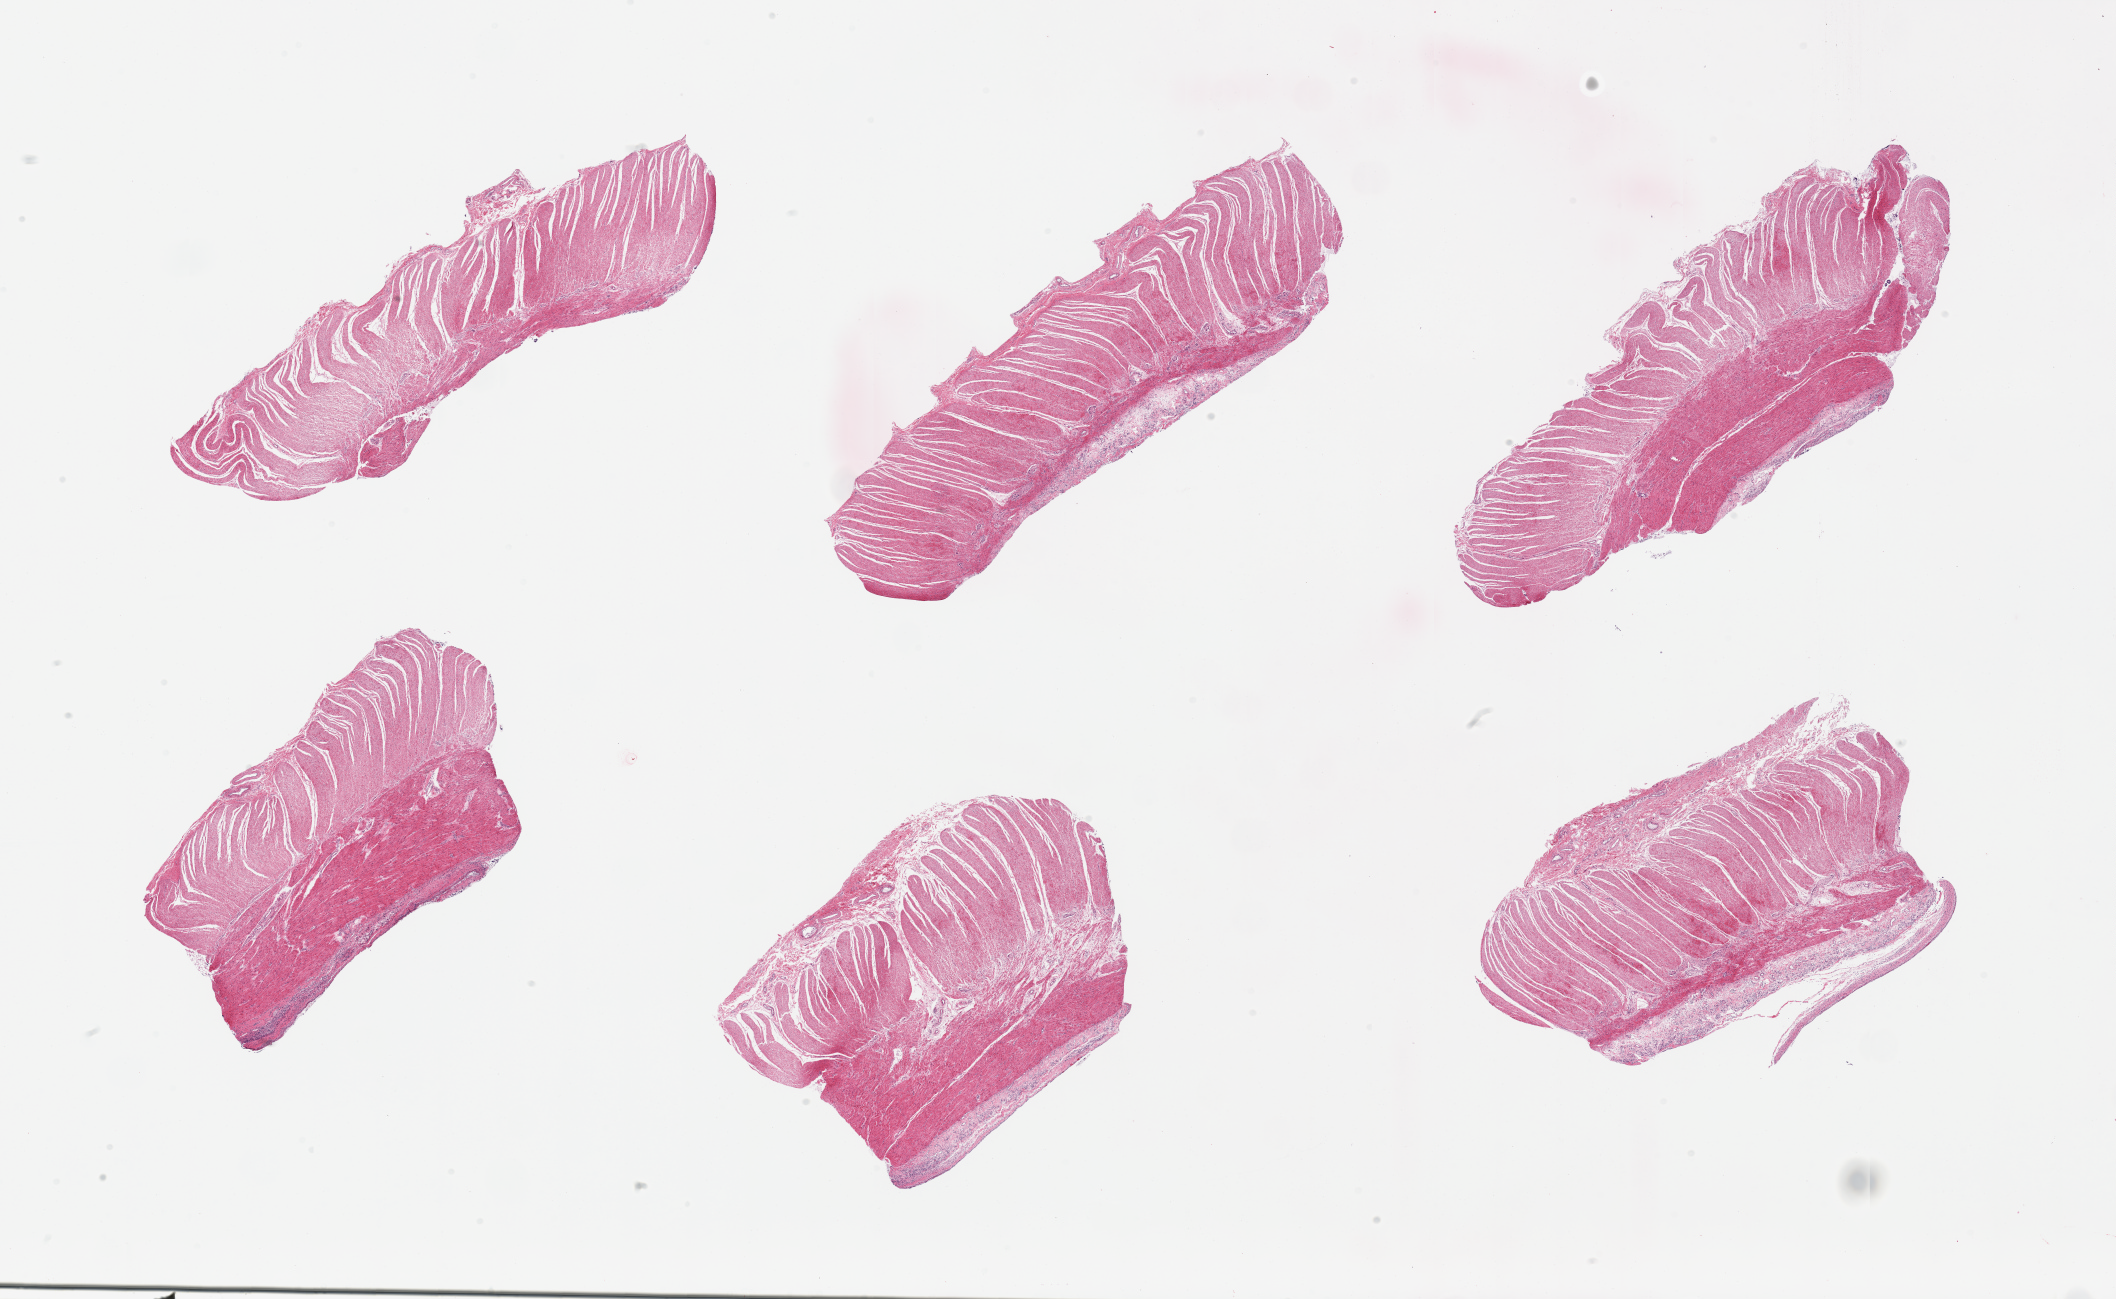
Whole-slide image, hematoxylin and eosin (H&E) stain — whole scanned area (about 33.5 x 20.5 mm) shown as a low-resolution overview. PAXgene-fixed, paraffin-embedded tissue. Target tissue: sigmoid colon. Tissue donor sample. Male donor.
Reviewer comment on this tissue sample: 6 pieces, mucscularis.